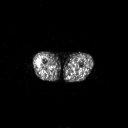
FDG PET of an extremity soft-tissue mass (from a PET/CT study), one axial slice. Slice 219 of 267 in the series (ordered by position). 3.27 mm slice thickness. 128 × 128 image matrix, field of view 700 × 700 mm. Patient: male, 43 years. From the clinical record (not read from this slice): histological type: poorly differentiated synovial sarcoma; grade: high; site of the primary tumour: right buttock.
Structures marked on this image (expert contour drawn on MRI and transferred to this co-registered scan by the dataset authors):
- gross tumour volume including surrounding oedema: bounding box <36,60,42,67> (left, top, right, bottom; pixels)